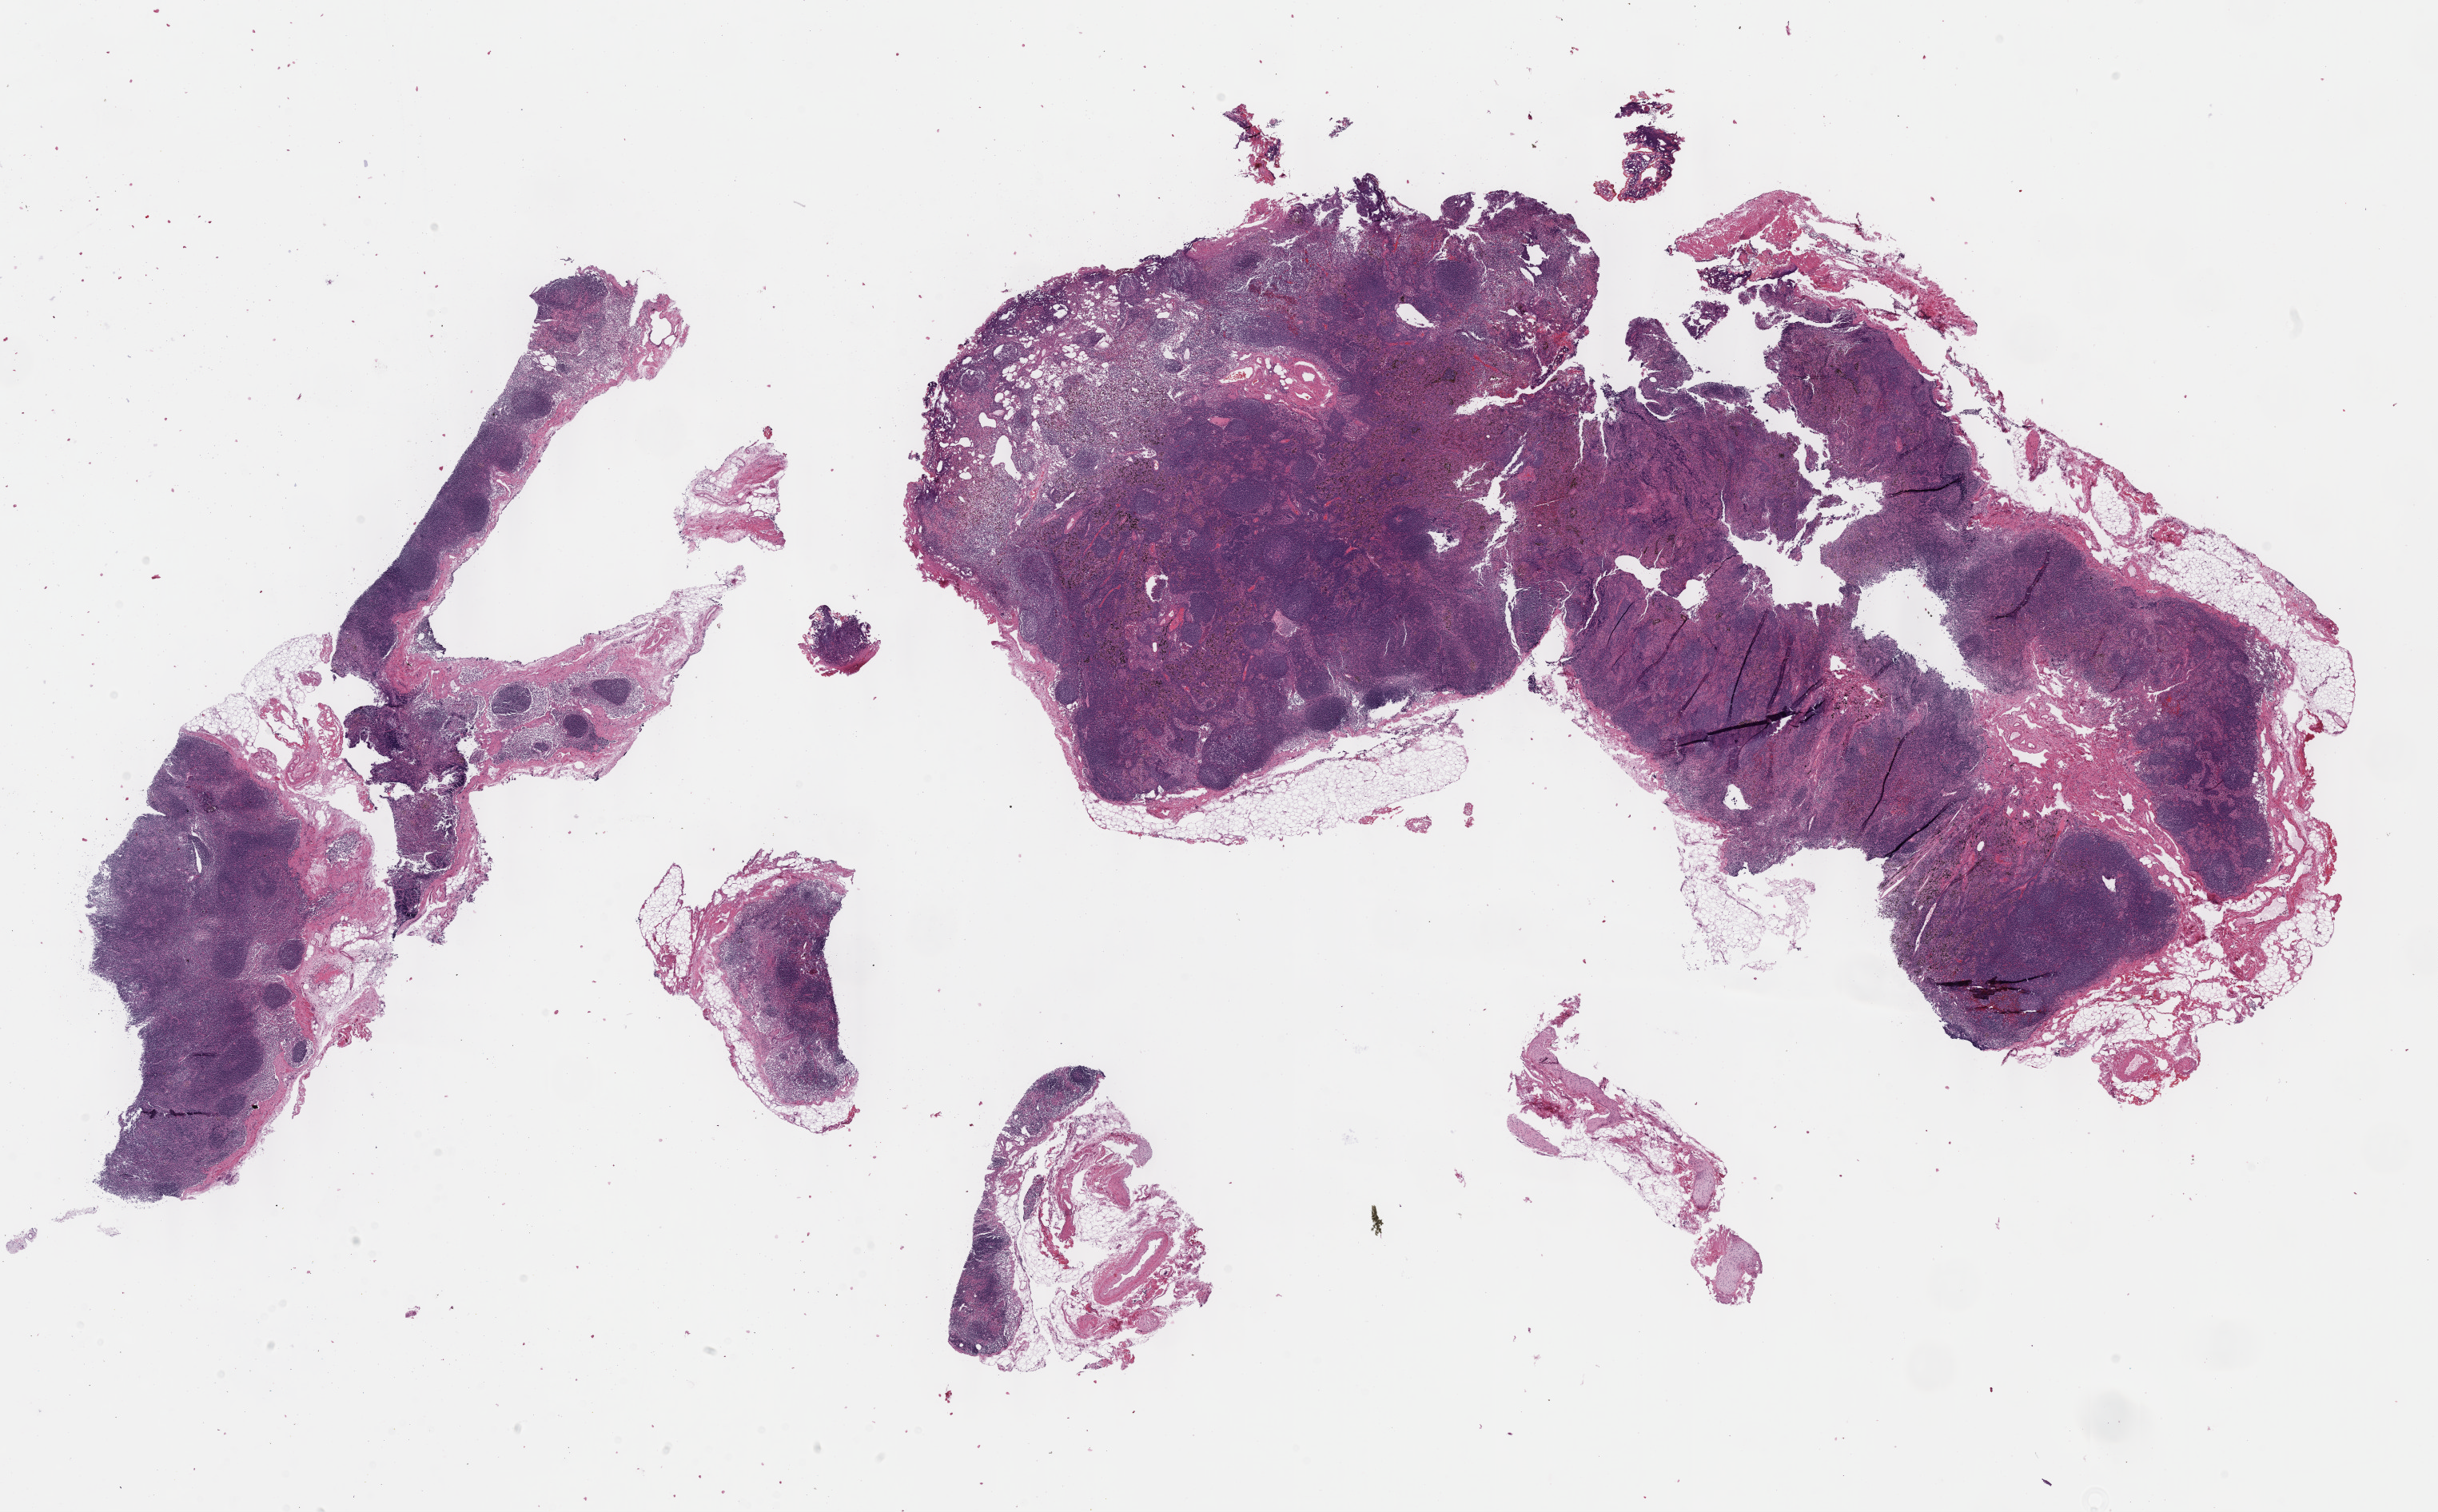
Digitized H&E-stained tissue section (whole slide), shown as a low-resolution overview of the whole scanned area (about 24.6 x 15.3 mm, slide scanned at 40x); formalin-fixed paraffin-embedded (FFPE) diagnostic section; primary tumour sample from the lung. Female patient; age at initial diagnosis 54 years.
- TNM: T2 N2 MX
- pathologic diagnosis: Adenocarcinoma, NOS (upper lobe, lung)
- laterality: left
- AJCC pathologic stage: IIIA (6th edition)